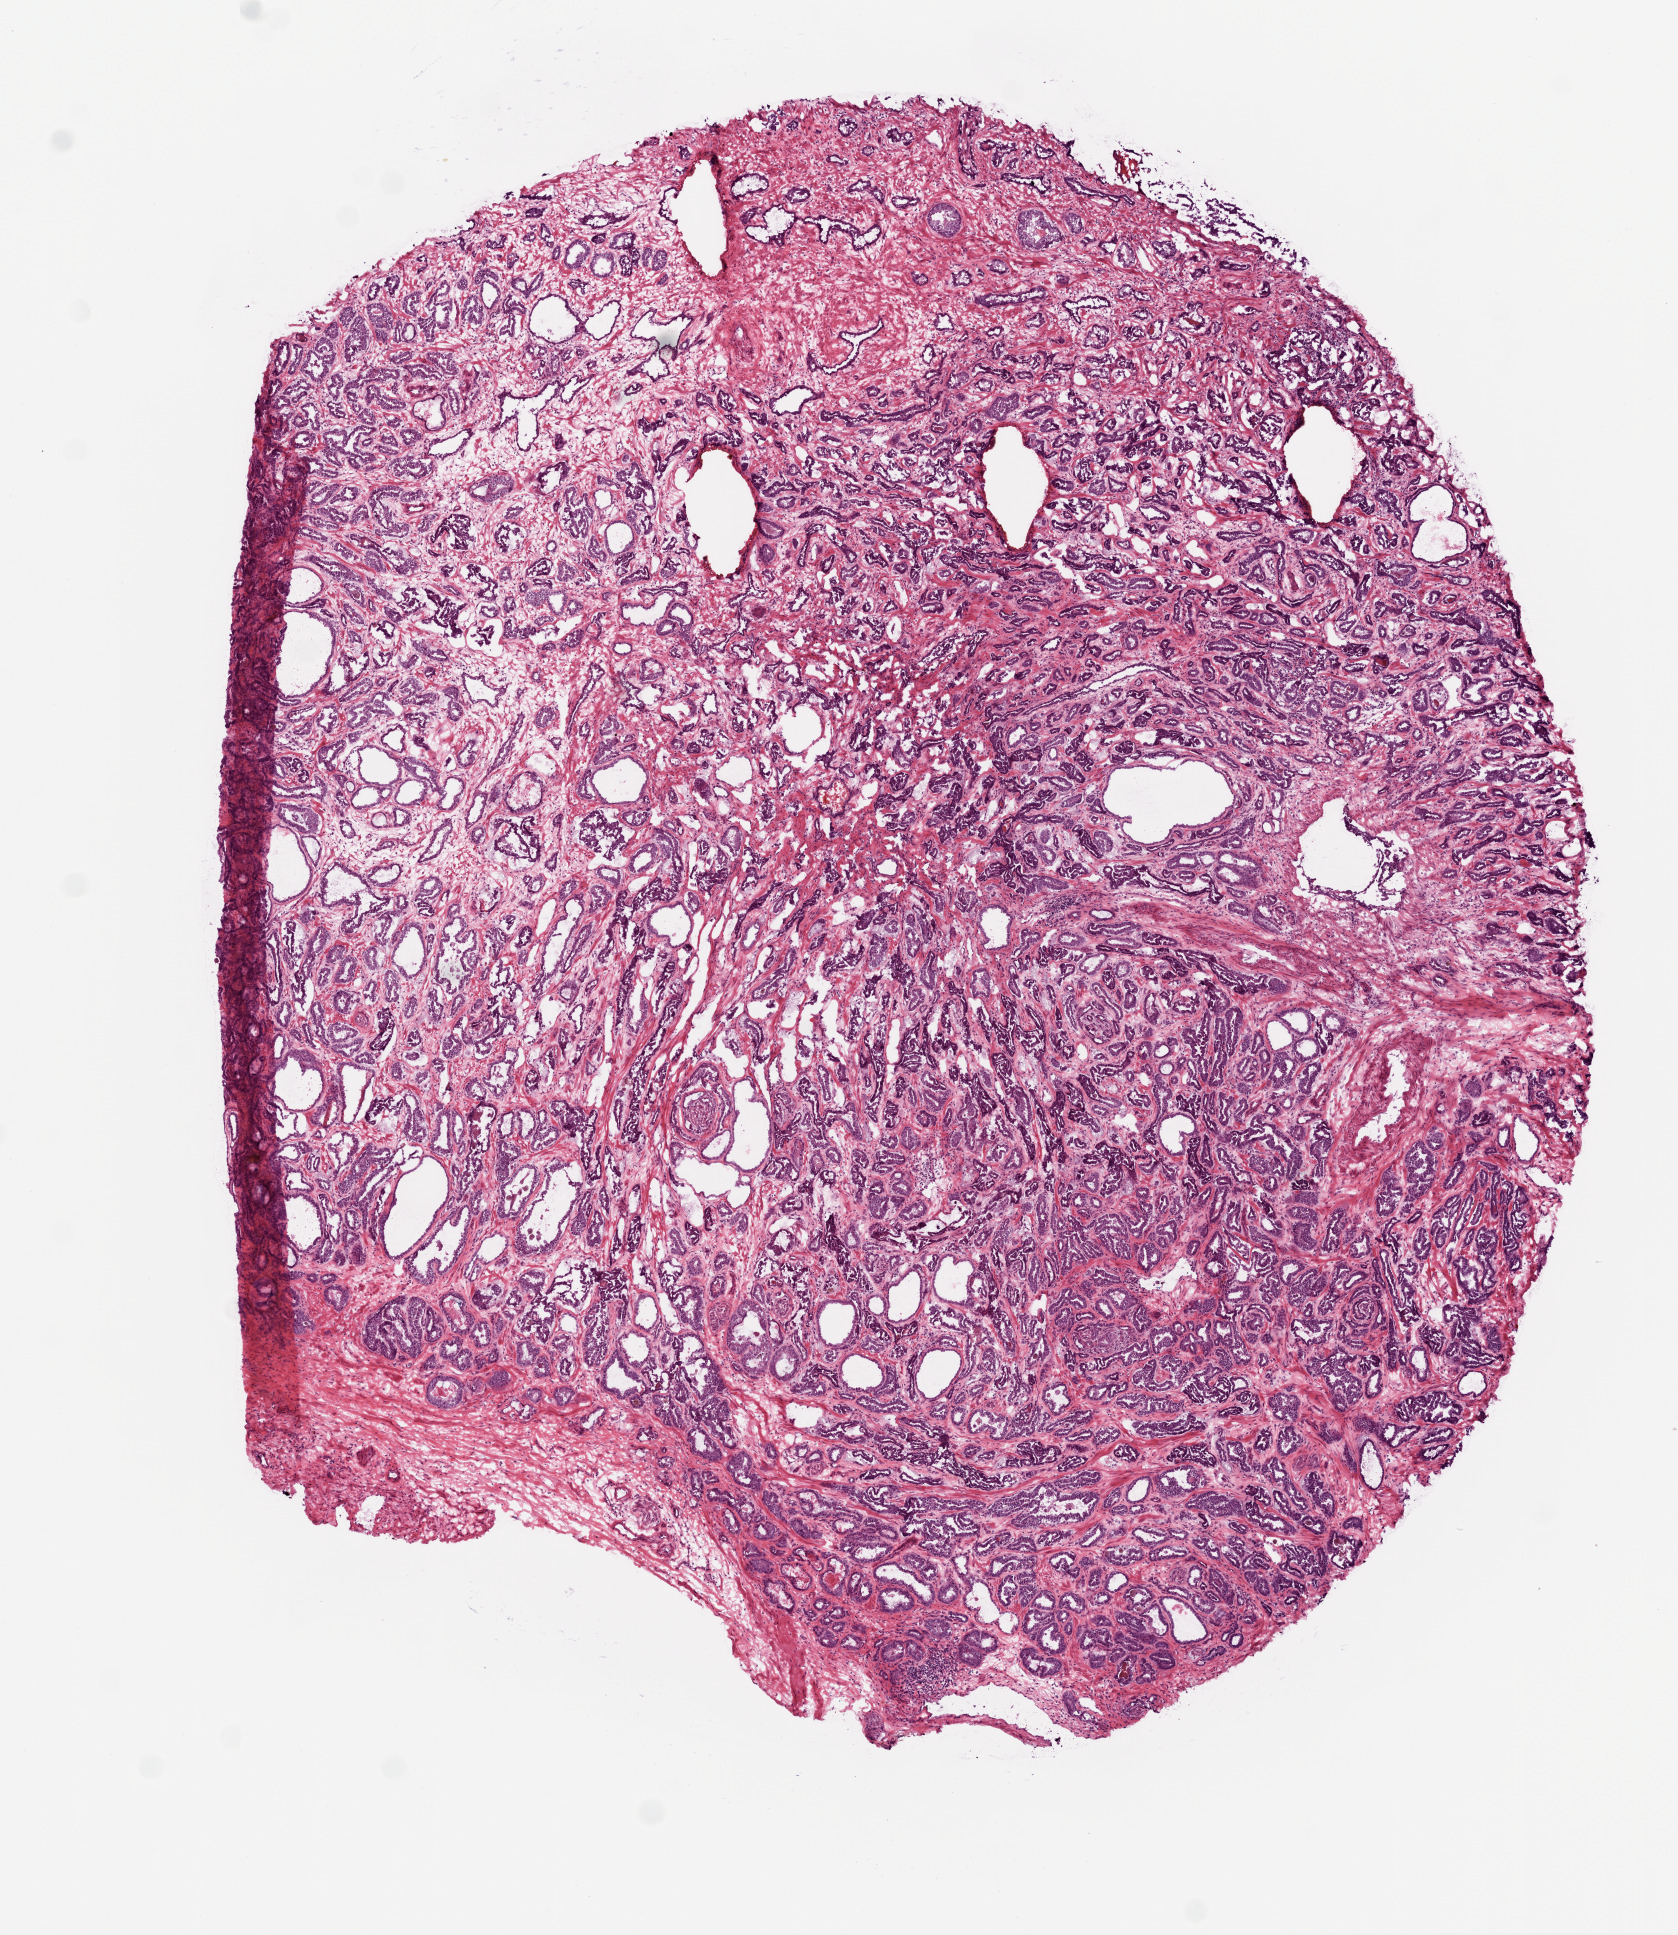
Digitized H&E-stained tissue section (whole slide) — whole scanned area (about 6.8 x 7.8 mm, acquisition: 20x scan) shown as a low-resolution overview; frozen section from the top of the tissue portion; prostate, primary tumour sample. Male patient; age at initial diagnosis 50 years. Gleason score: 7 (3+4). Composition of this section per pathologist review: tumour cells 85%, tumour nuclei 85%, normal cells 0%, stromal cells 15%, necrosis 0%.
Pathologic diagnosis: Acinar cell carcinoma (prostate gland).